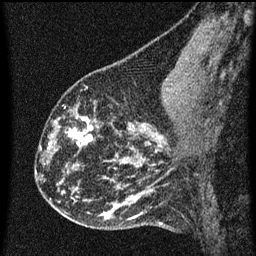
Breast MRI (dynamic contrast-enhanced), one sagittal slice. Position 23 of 60 along the scan axis. Dynamic contrast-enhanced series, image 2 of 3 at this slice position (ordered by acquisition). 1.5 T. TE 4.2 ms, TR 8 ms. 256 × 256 image matrix. Female patient, age 43 years.
Annotated regions visible in this slice (semi-automatic segmentation, software-assisted and operator-edited):
- analysis volume of interest (the breast-tissue region the enhancement analysis was run in; not a lesion): bounding box (x1, y1, x2, y2) in pixels: (55, 104, 104, 153)
- tumour enhancement mask (voxels above the 70 % enhancement threshold inside the analysis volume of interest): (69, 116, 93, 147)